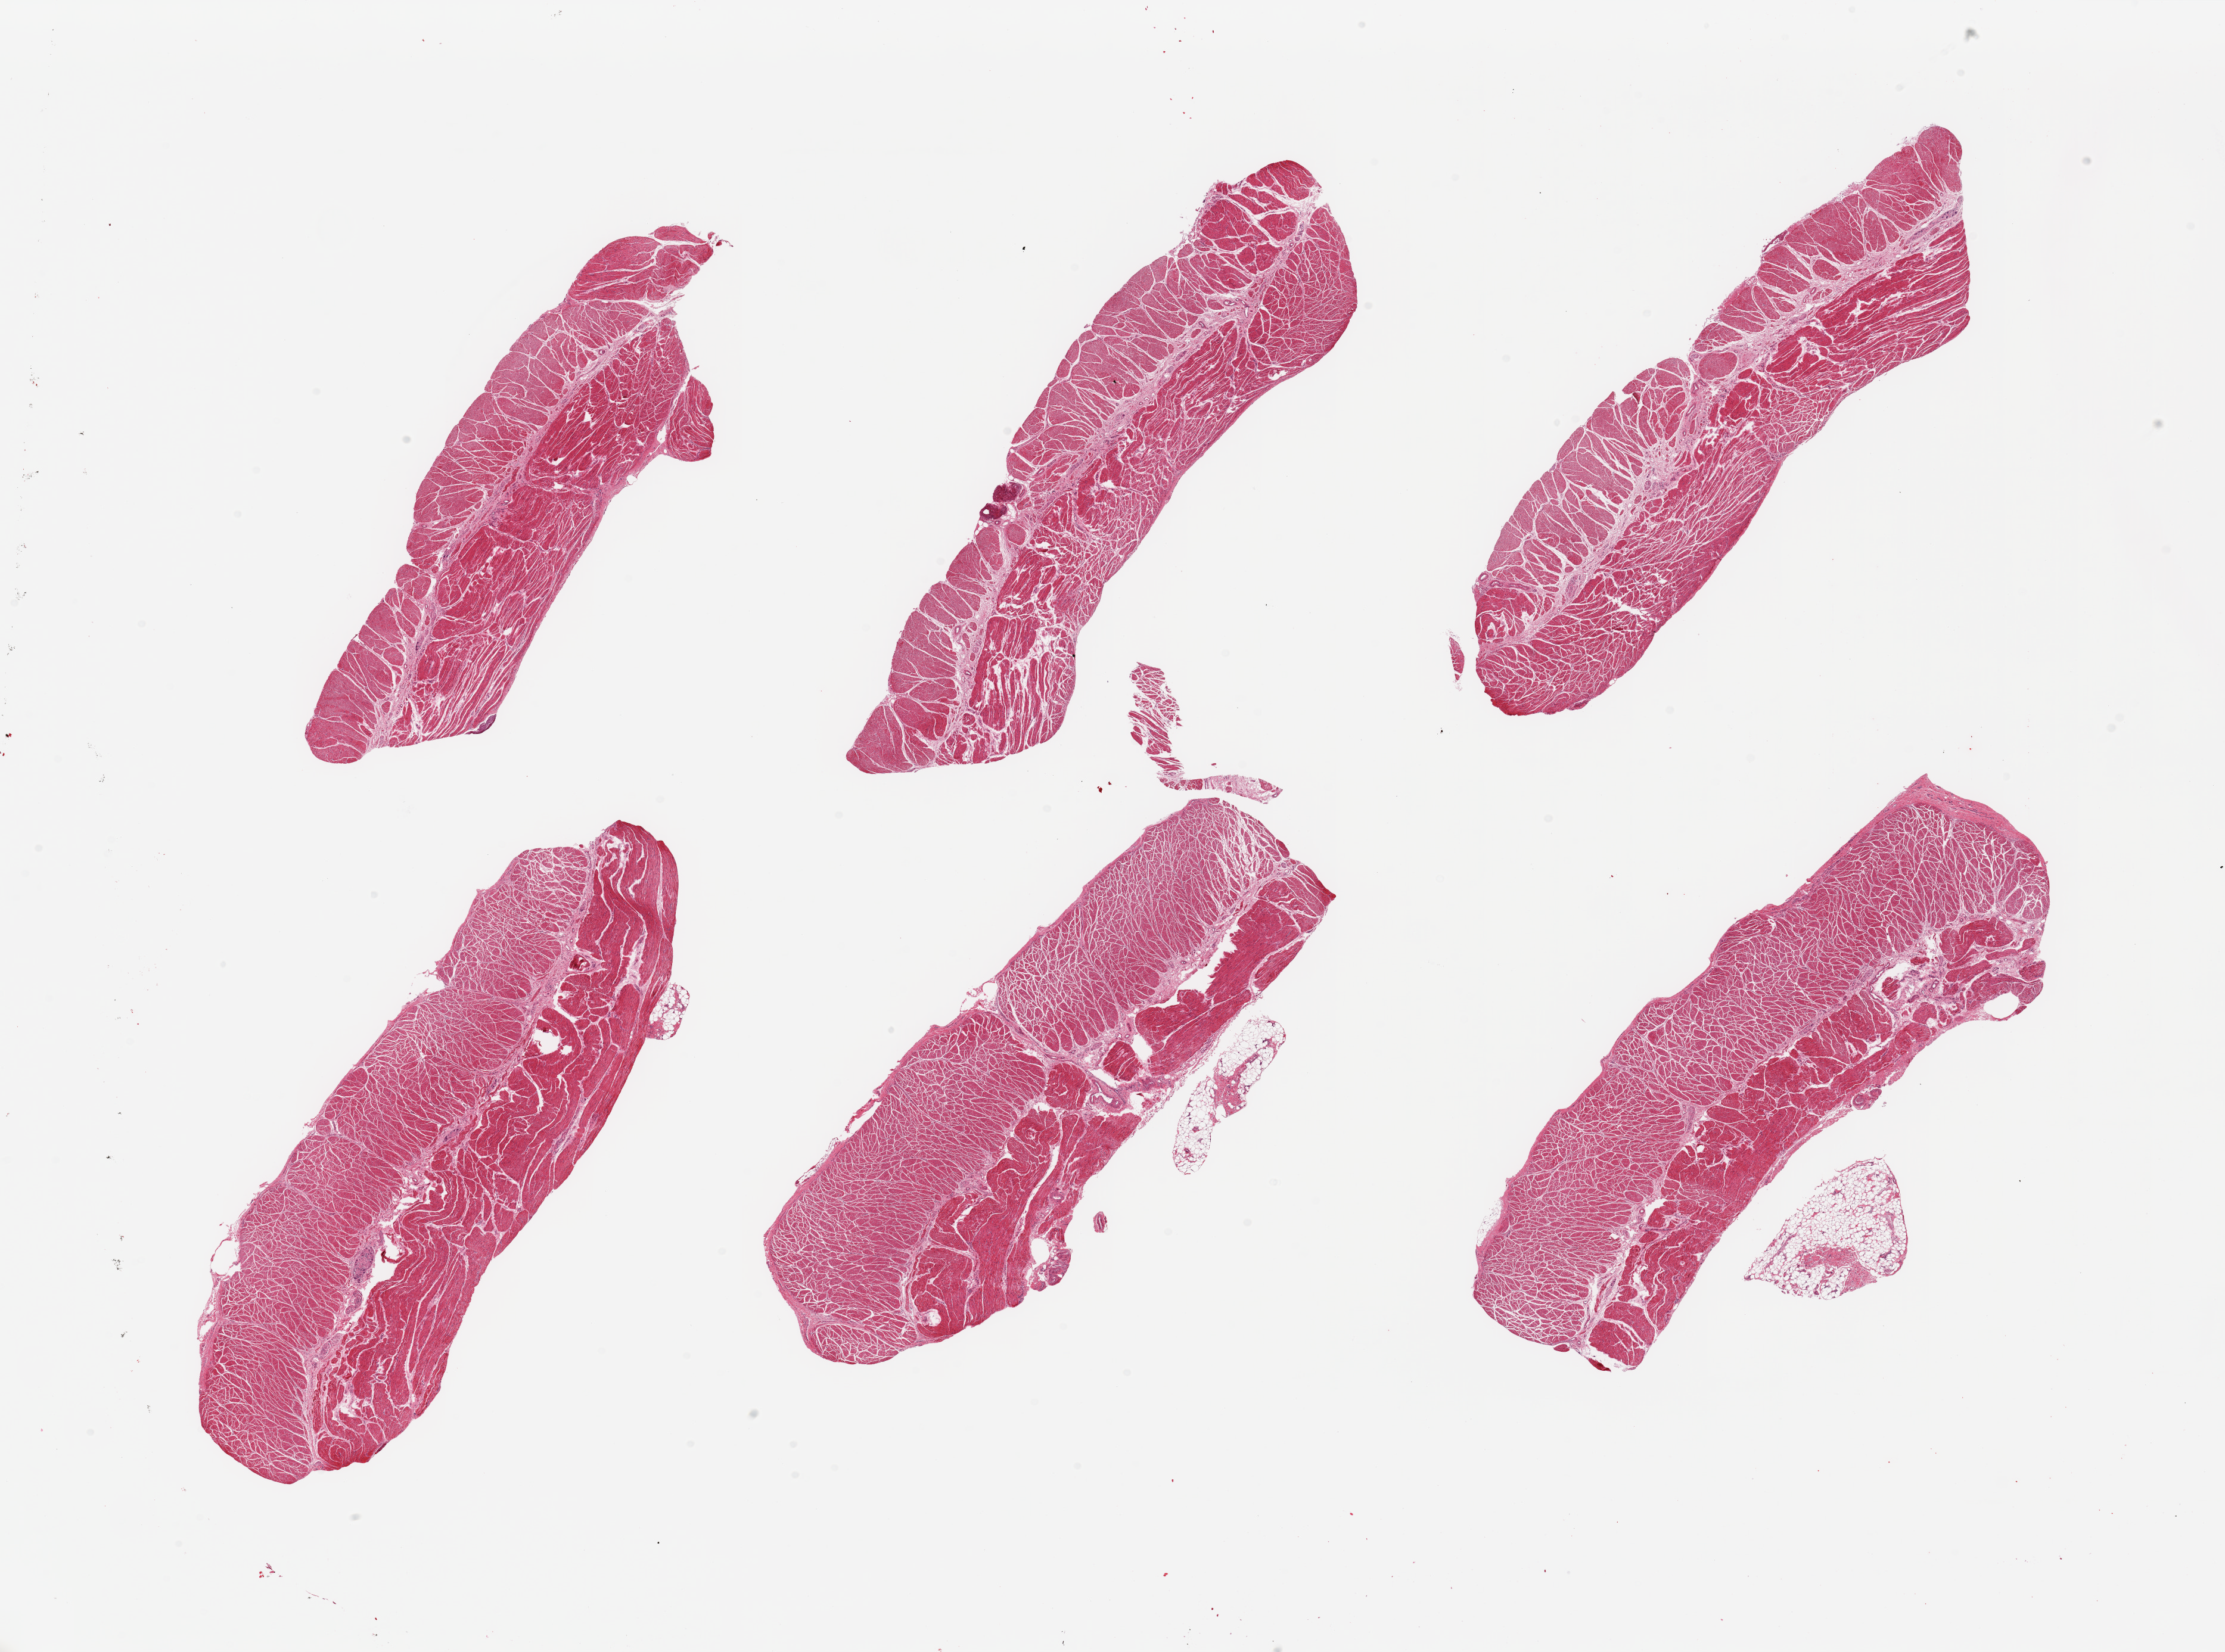
Whole-slide image, haematoxylin and eosin stain, whole scanned area (about 29.5 x 21.9 mm, acquisition: 20x scan) shown as a low-resolution overview. PAXgene-fixed paraffin-embedded (PFPE) section. Section of esophageal muscle (target tissue). Donor tissue sample. Donor: male.
Pathologist's review note for this sample: 6 pieces; well dissected muscle.